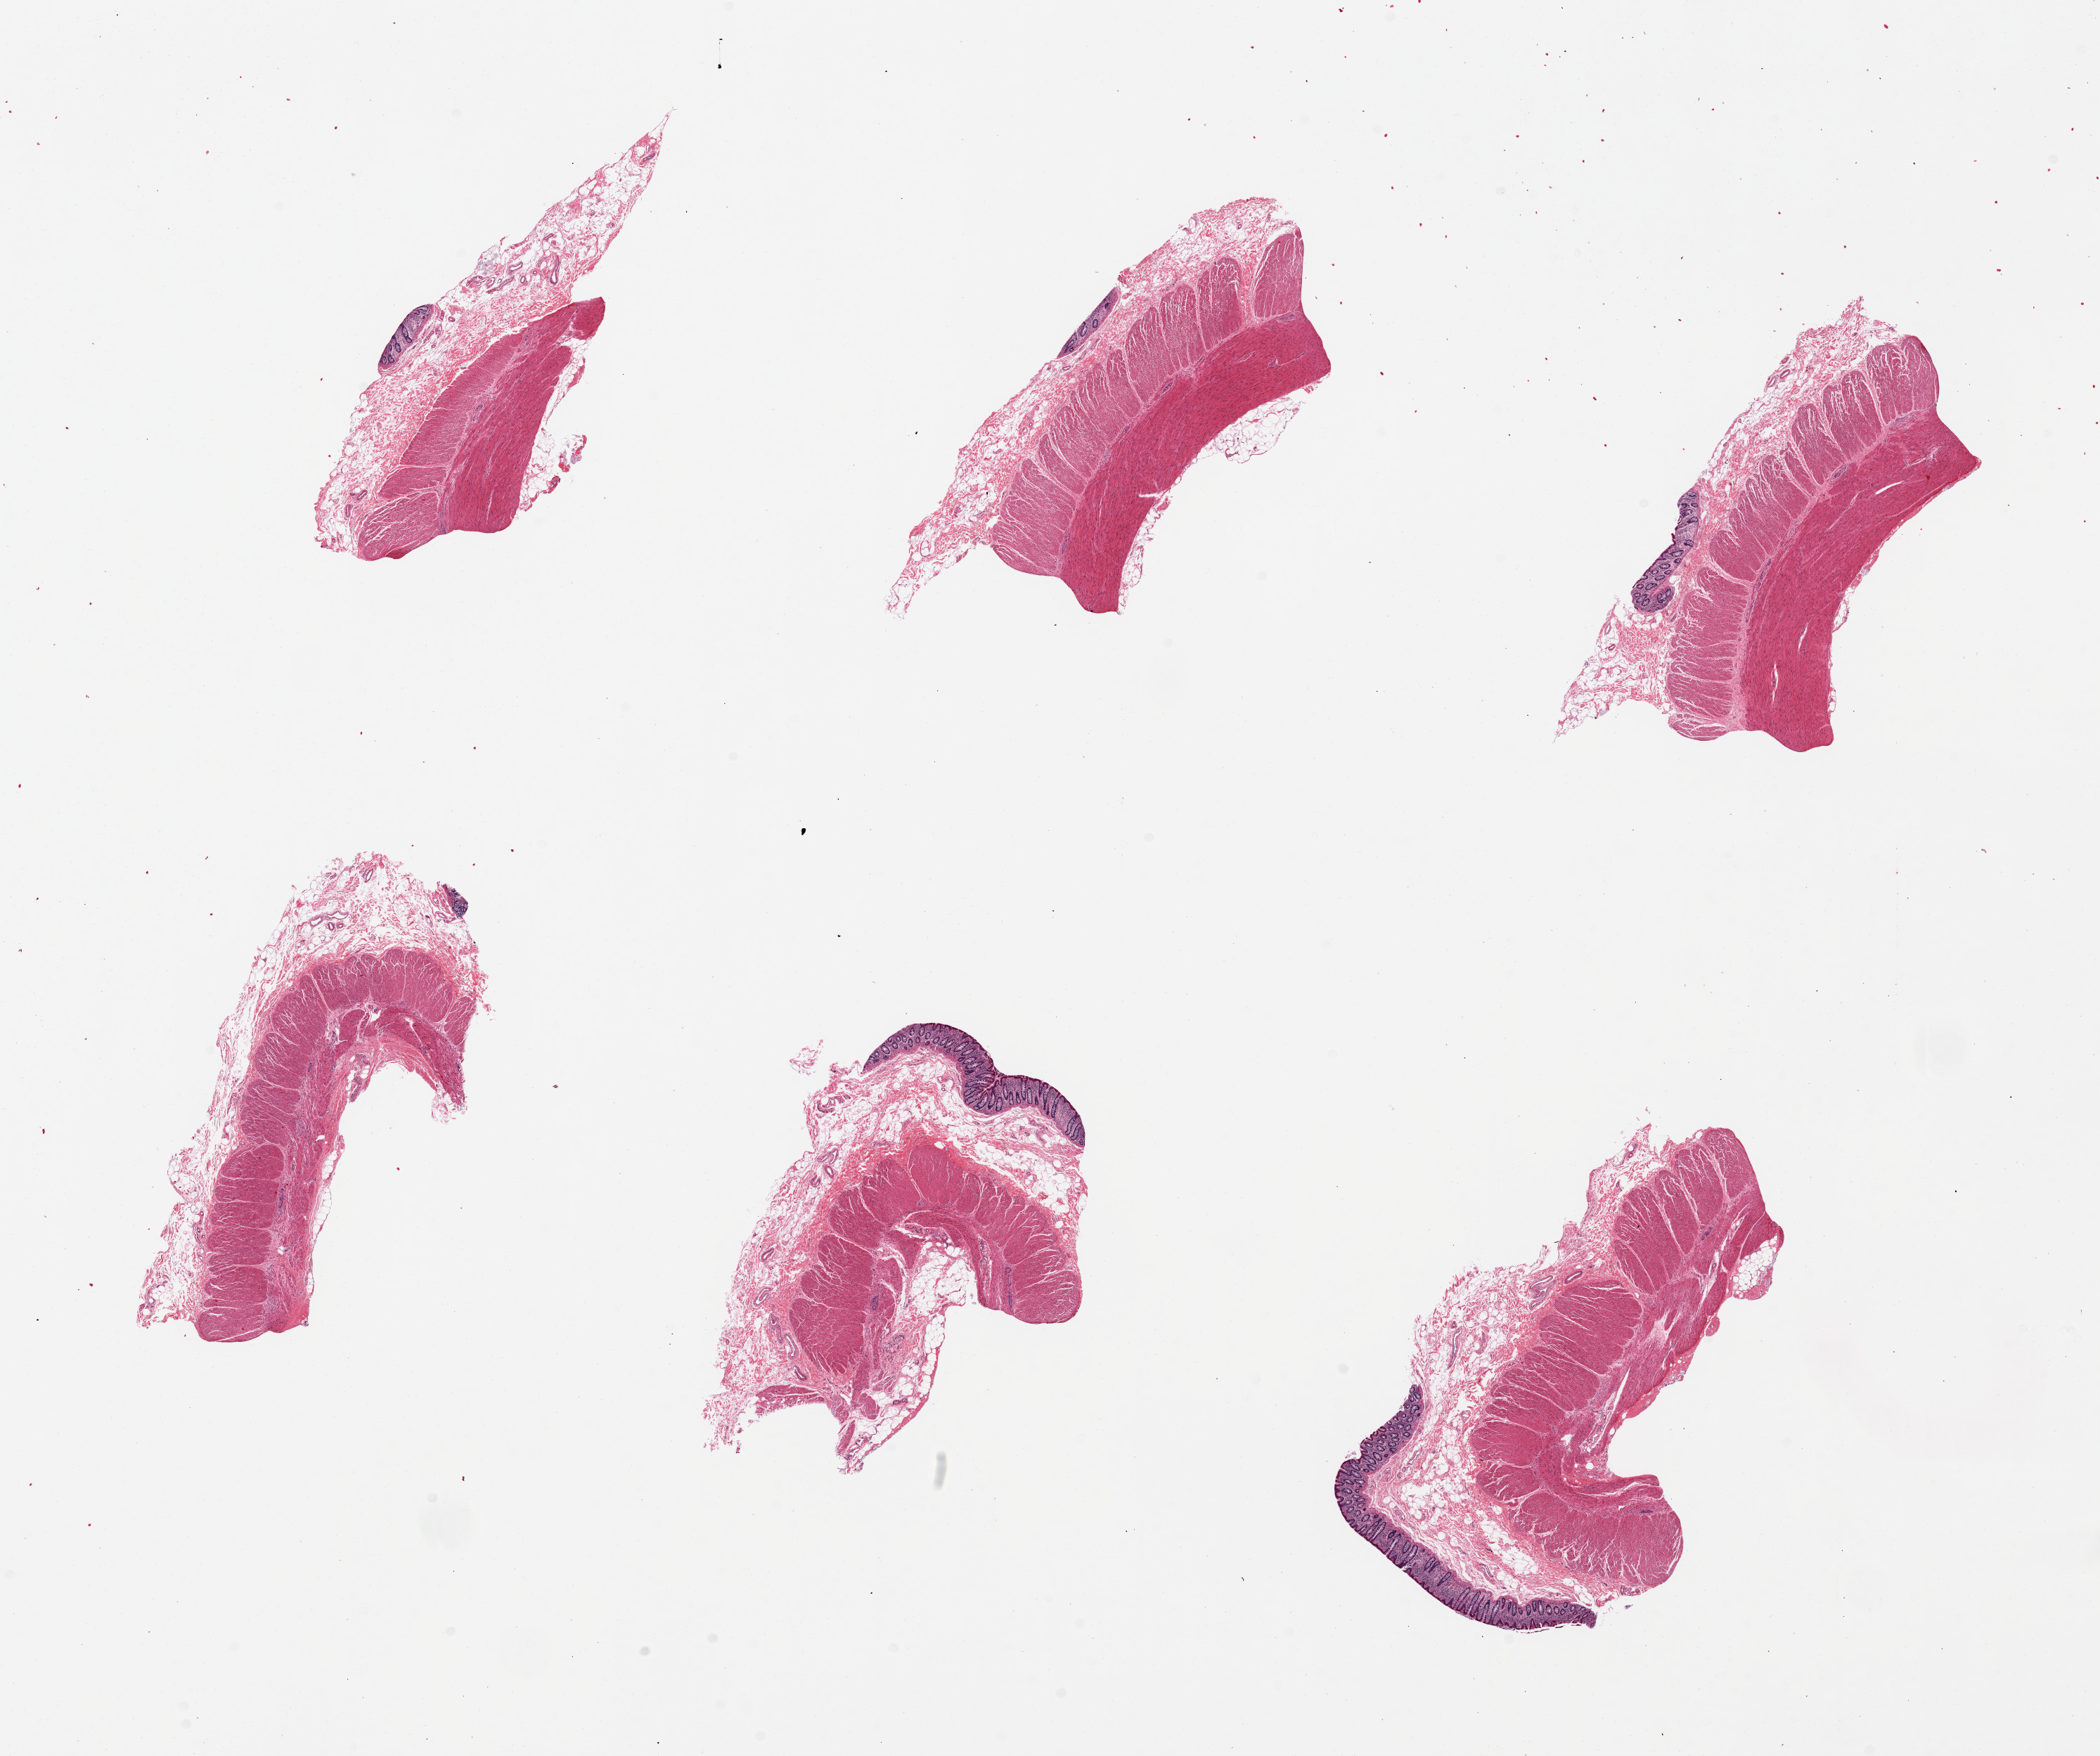
H&E whole-slide image, brightfield — shown as a low-resolution overview of the whole scanned area (about 23.6 x 19.8 mm, acquisition: 20x scan); PAXgene-fixed paraffin-embedded (PFPE) section; sampled site (target tissue): transverse colon; tissue donor sample. Female donor.
Review note (as recorded): 6 pieces, each containing muscularis and varying amounts of mucosa.